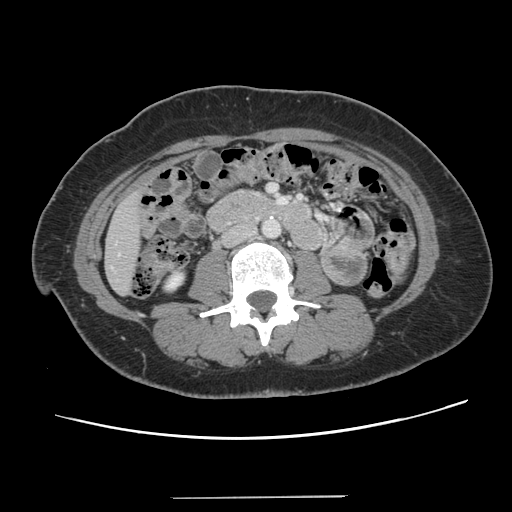
Contrast-enhanced abdominal CT, one axial slice. Position 28 of 141 along the scan axis. Intravenous contrast given. Soft-tissue window (W 400 / L 40 HU). 2.5 mm slice thickness. 512 × 512 image matrix, field of view 366 × 366 mm. Female patient, age 53 years. From the clinical record (not read from this slice): diagnosis: colorectal cancer liver metastases, imaged before liver resection; multiple liver metastases: no; largest metastasis: 14.5 cm; disease in both lobes: yes.
Outlined on this slice (outlined manually by an expert reader):
- liver: bounding box [x1, y1, x2, y2] px = [106, 197, 141, 293]
- planned liver remnant (the part of the liver to remain after resection): [106, 205, 141, 293]